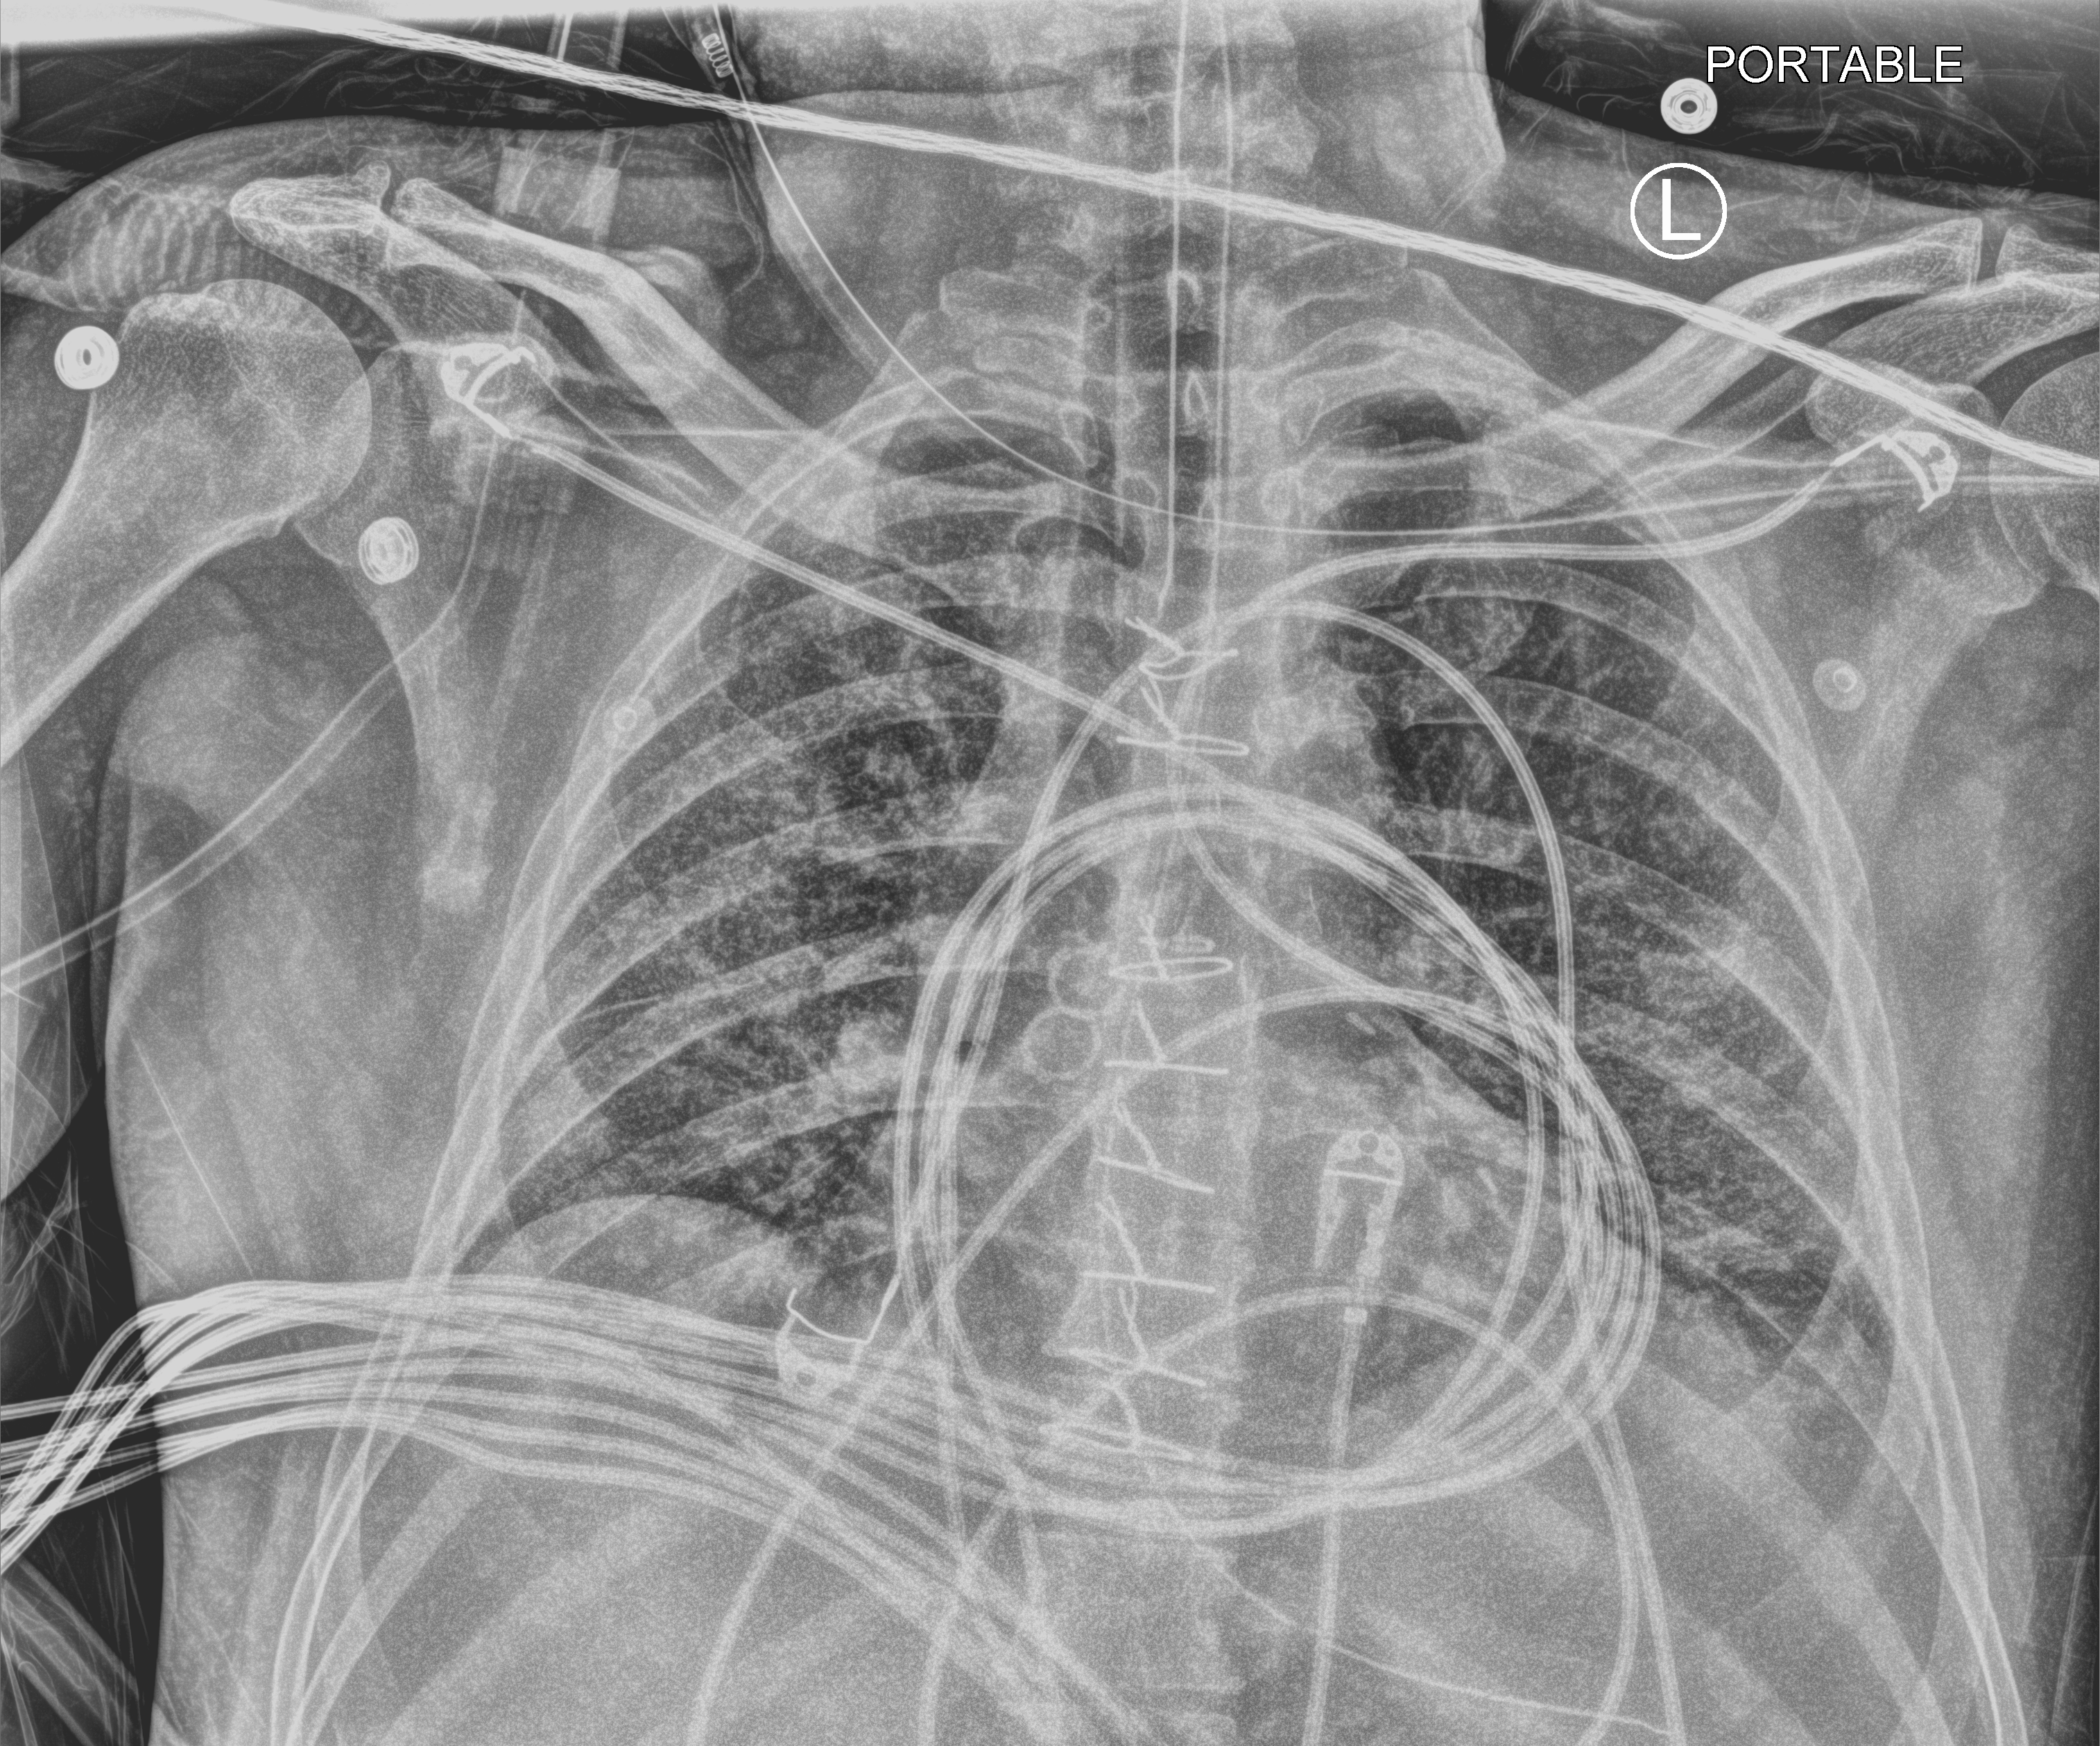
Bedside chest radiograph (computed radiography); anteroposterior (AP) projection. Patient hospitalised with COVID-19; male, aged 18–59 years.
Admission-level facts for this patient (not findings on this image; timing relative to this image not recorded):
- length of hospital stay: 63 days
- smoking status (admission record): former
- admitted to intensive care during this hospital stay: yes